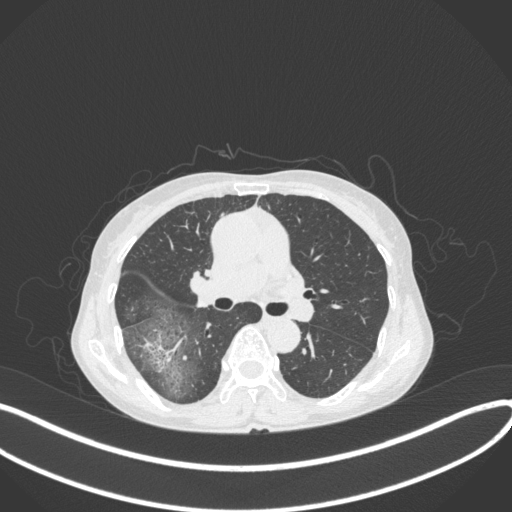
Chest CT, one axial slice. Slice 234 of 379 in the series (ordered by position). Lung window (W 1500 / L -600 HU). 1 mm slice thickness. 512 × 512 image matrix. Patient: female, 69 years. From the clinical record (not read from this slice): clinical TNM (as recorded): T1b N0 M0; histopathological grade: G2-3.
Structures marked on this image (bounding box drawn by a radiologist):
- lung tumour (recorded histology: adenocarcinoma): bounding box <142,331,185,376> (left, top, right, bottom; pixels)